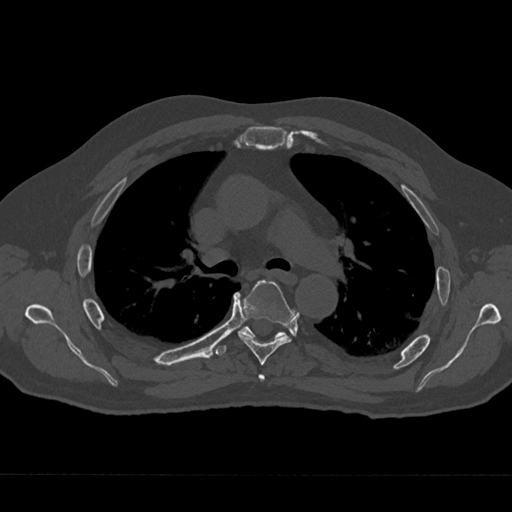
CT including the spine, one axial slice; slice 459 of 797 in the series (ordered by position); reconstruction kernel Br40s/3; bone window (W 1800 / L 400 HU); 512 × 512 image matrix, field of view 377 × 377 mm. Male patient, age 75 years. From the clinical record (not read from this slice): primary cancer: renal.
Structures marked on this image (semi-automatic segmentation, software-assisted and operator-edited):
- T4 vertebra: bounding box <258,374,265,381> (left, top, right, bottom; pixels)
- T5 vertebra: <238,280,293,365>
- T6 vertebra: <217,326,286,355>